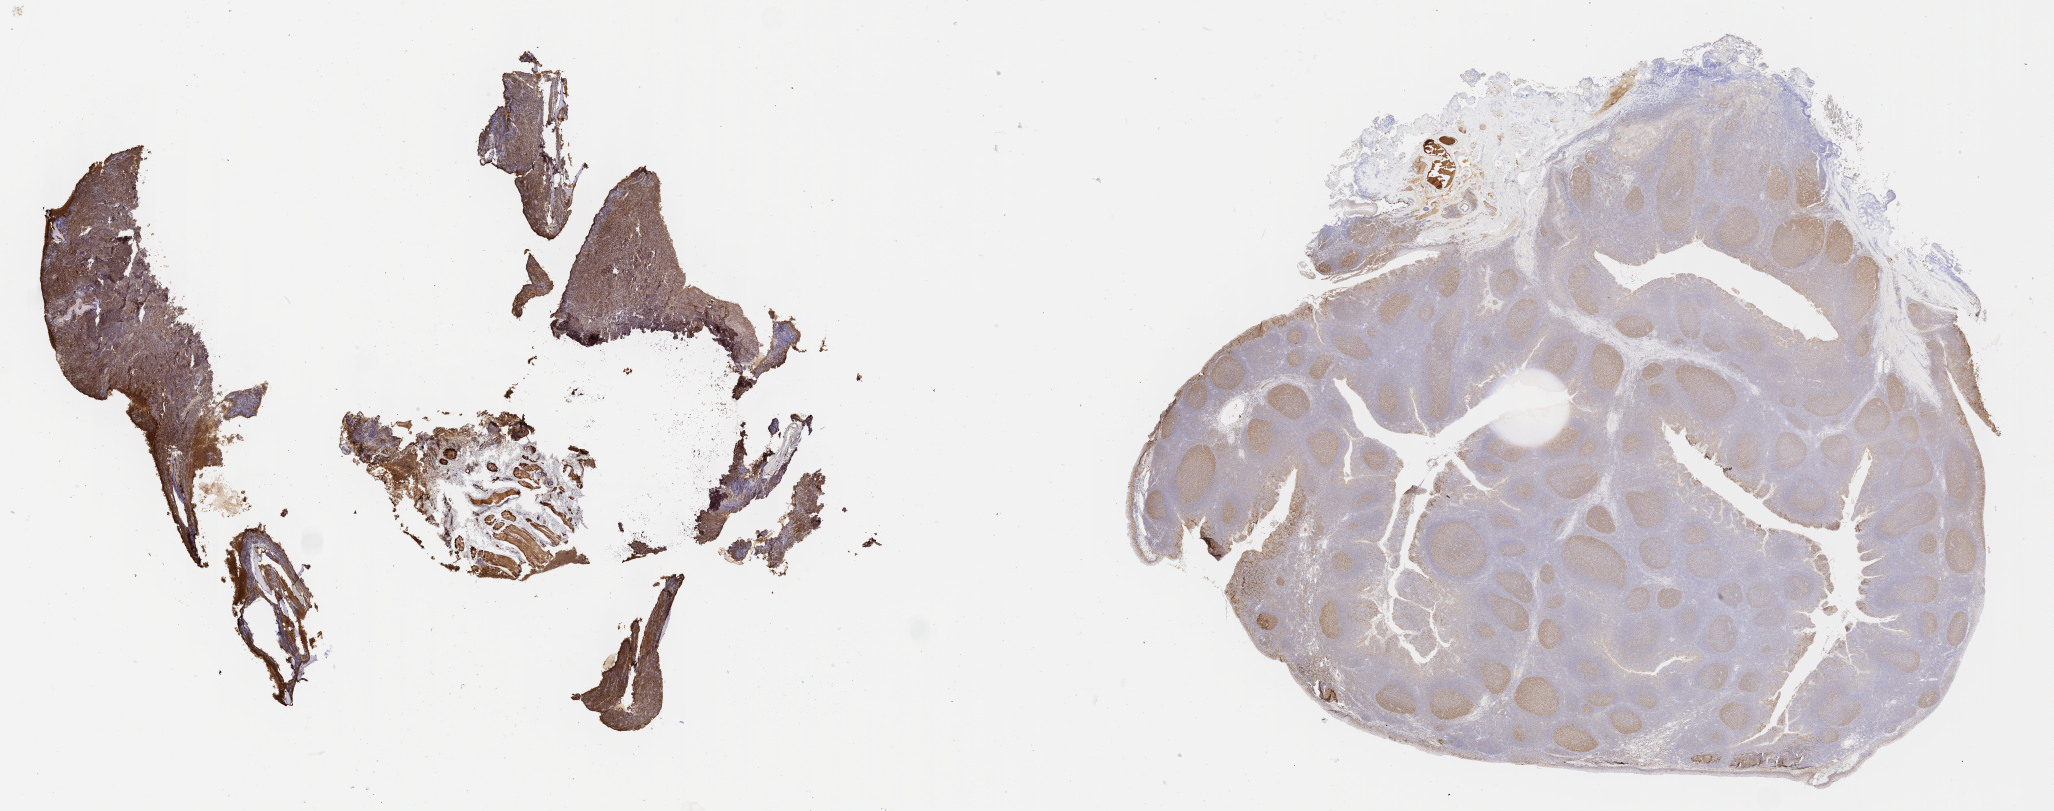
Whole-slide image, immunohistochemical stain for BCL6, low-resolution overview of the scanned area, about 33.2 x 13.1 mm, specimen: tumor tissue, site: cranium. Patient: male, age at initial diagnosis 8 years.
* histologic diagnosis: Burkitt lymphoma, NOS